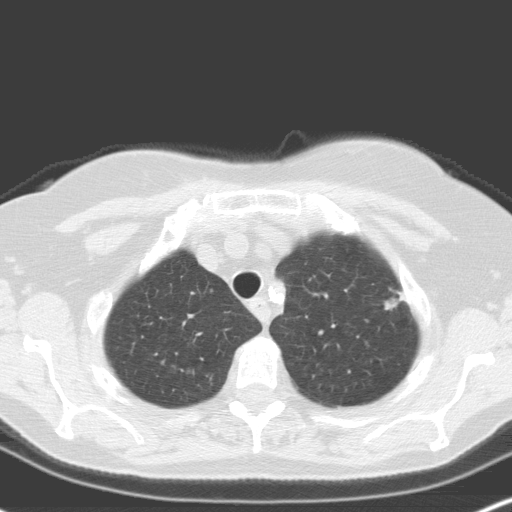
Low-dose screening chest CT, one axial slice; slice 140 of 160 in the series (ordered by position); lung window (W 1500 / L -600 HU); 3.2 mm slice thickness; 512 × 512 image matrix, field of view 316 × 316 mm.
Annotated regions visible in this slice (outlined manually by an expert reader):
- lesion 2 (nodule): bounding box (x1, y1, x2, y2) in pixels: (385, 294, 407, 310)